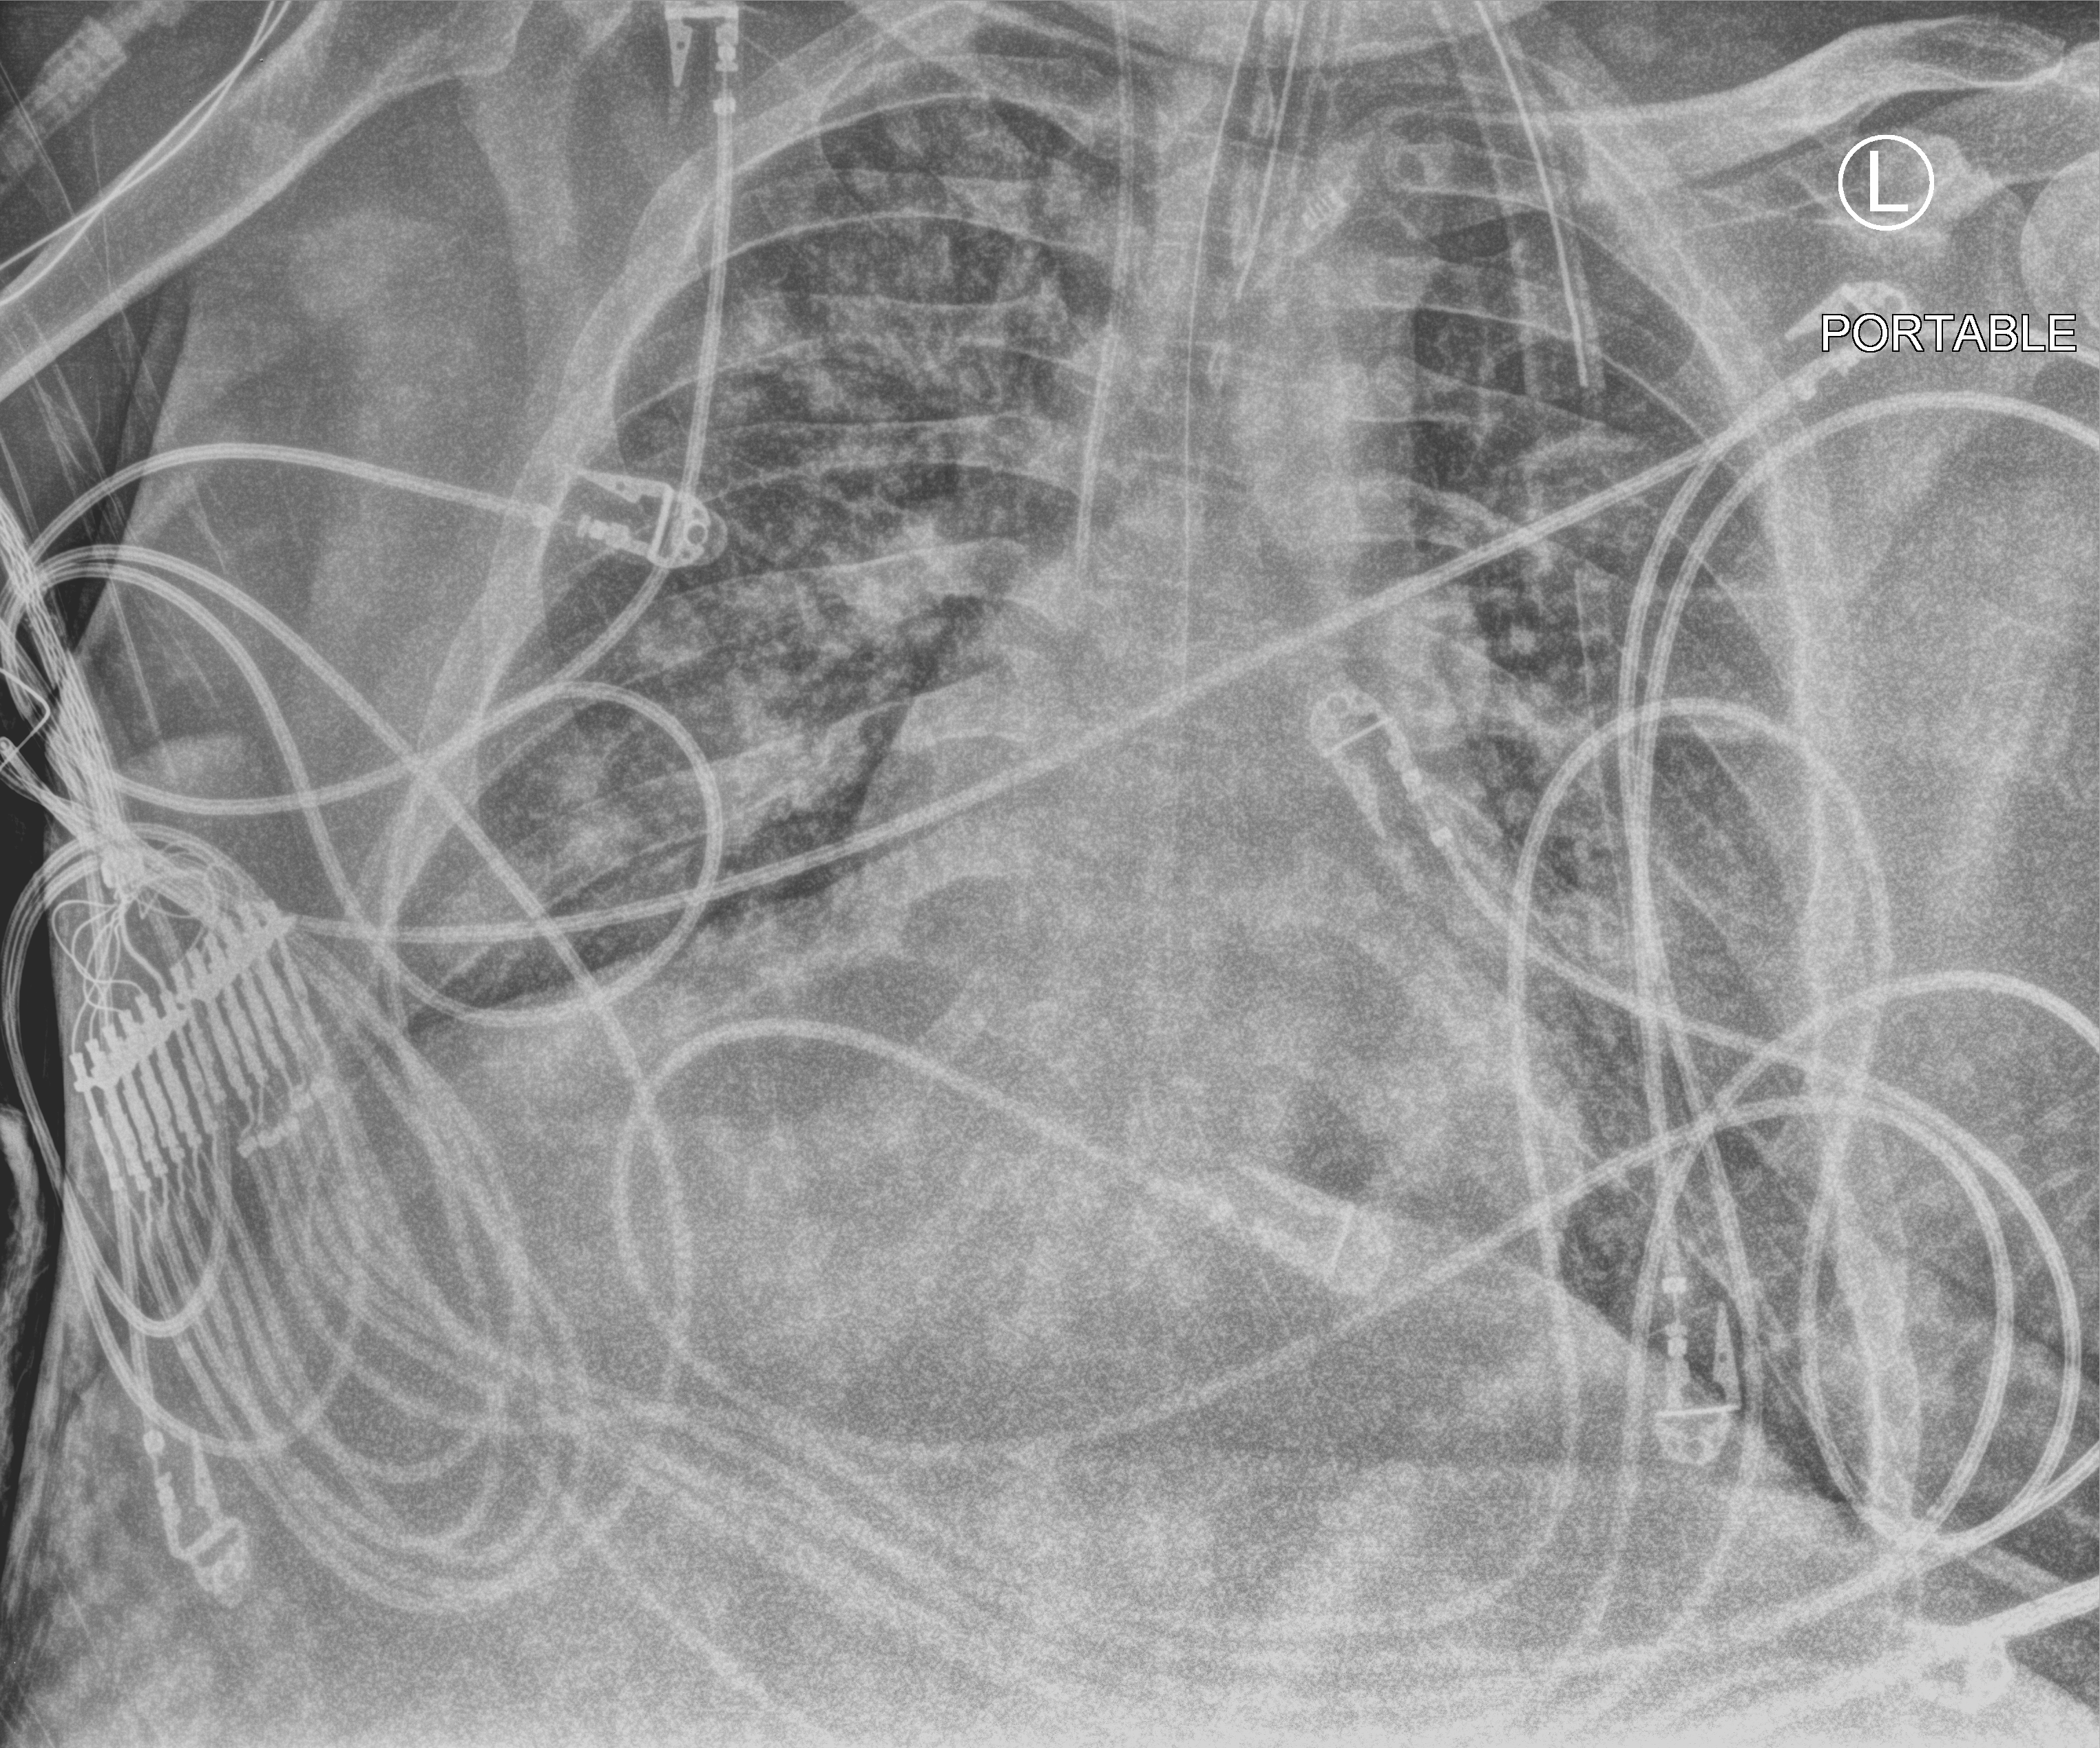
Bedside chest radiograph (computed radiography), anteroposterior (AP) projection. Adult patient hospitalised with COVID-19, age 18–59 years.
Hospital-stay facts (about this admission, not read from this image; timing relative to this image not recorded):
- mechanically ventilated during this hospital stay: yes